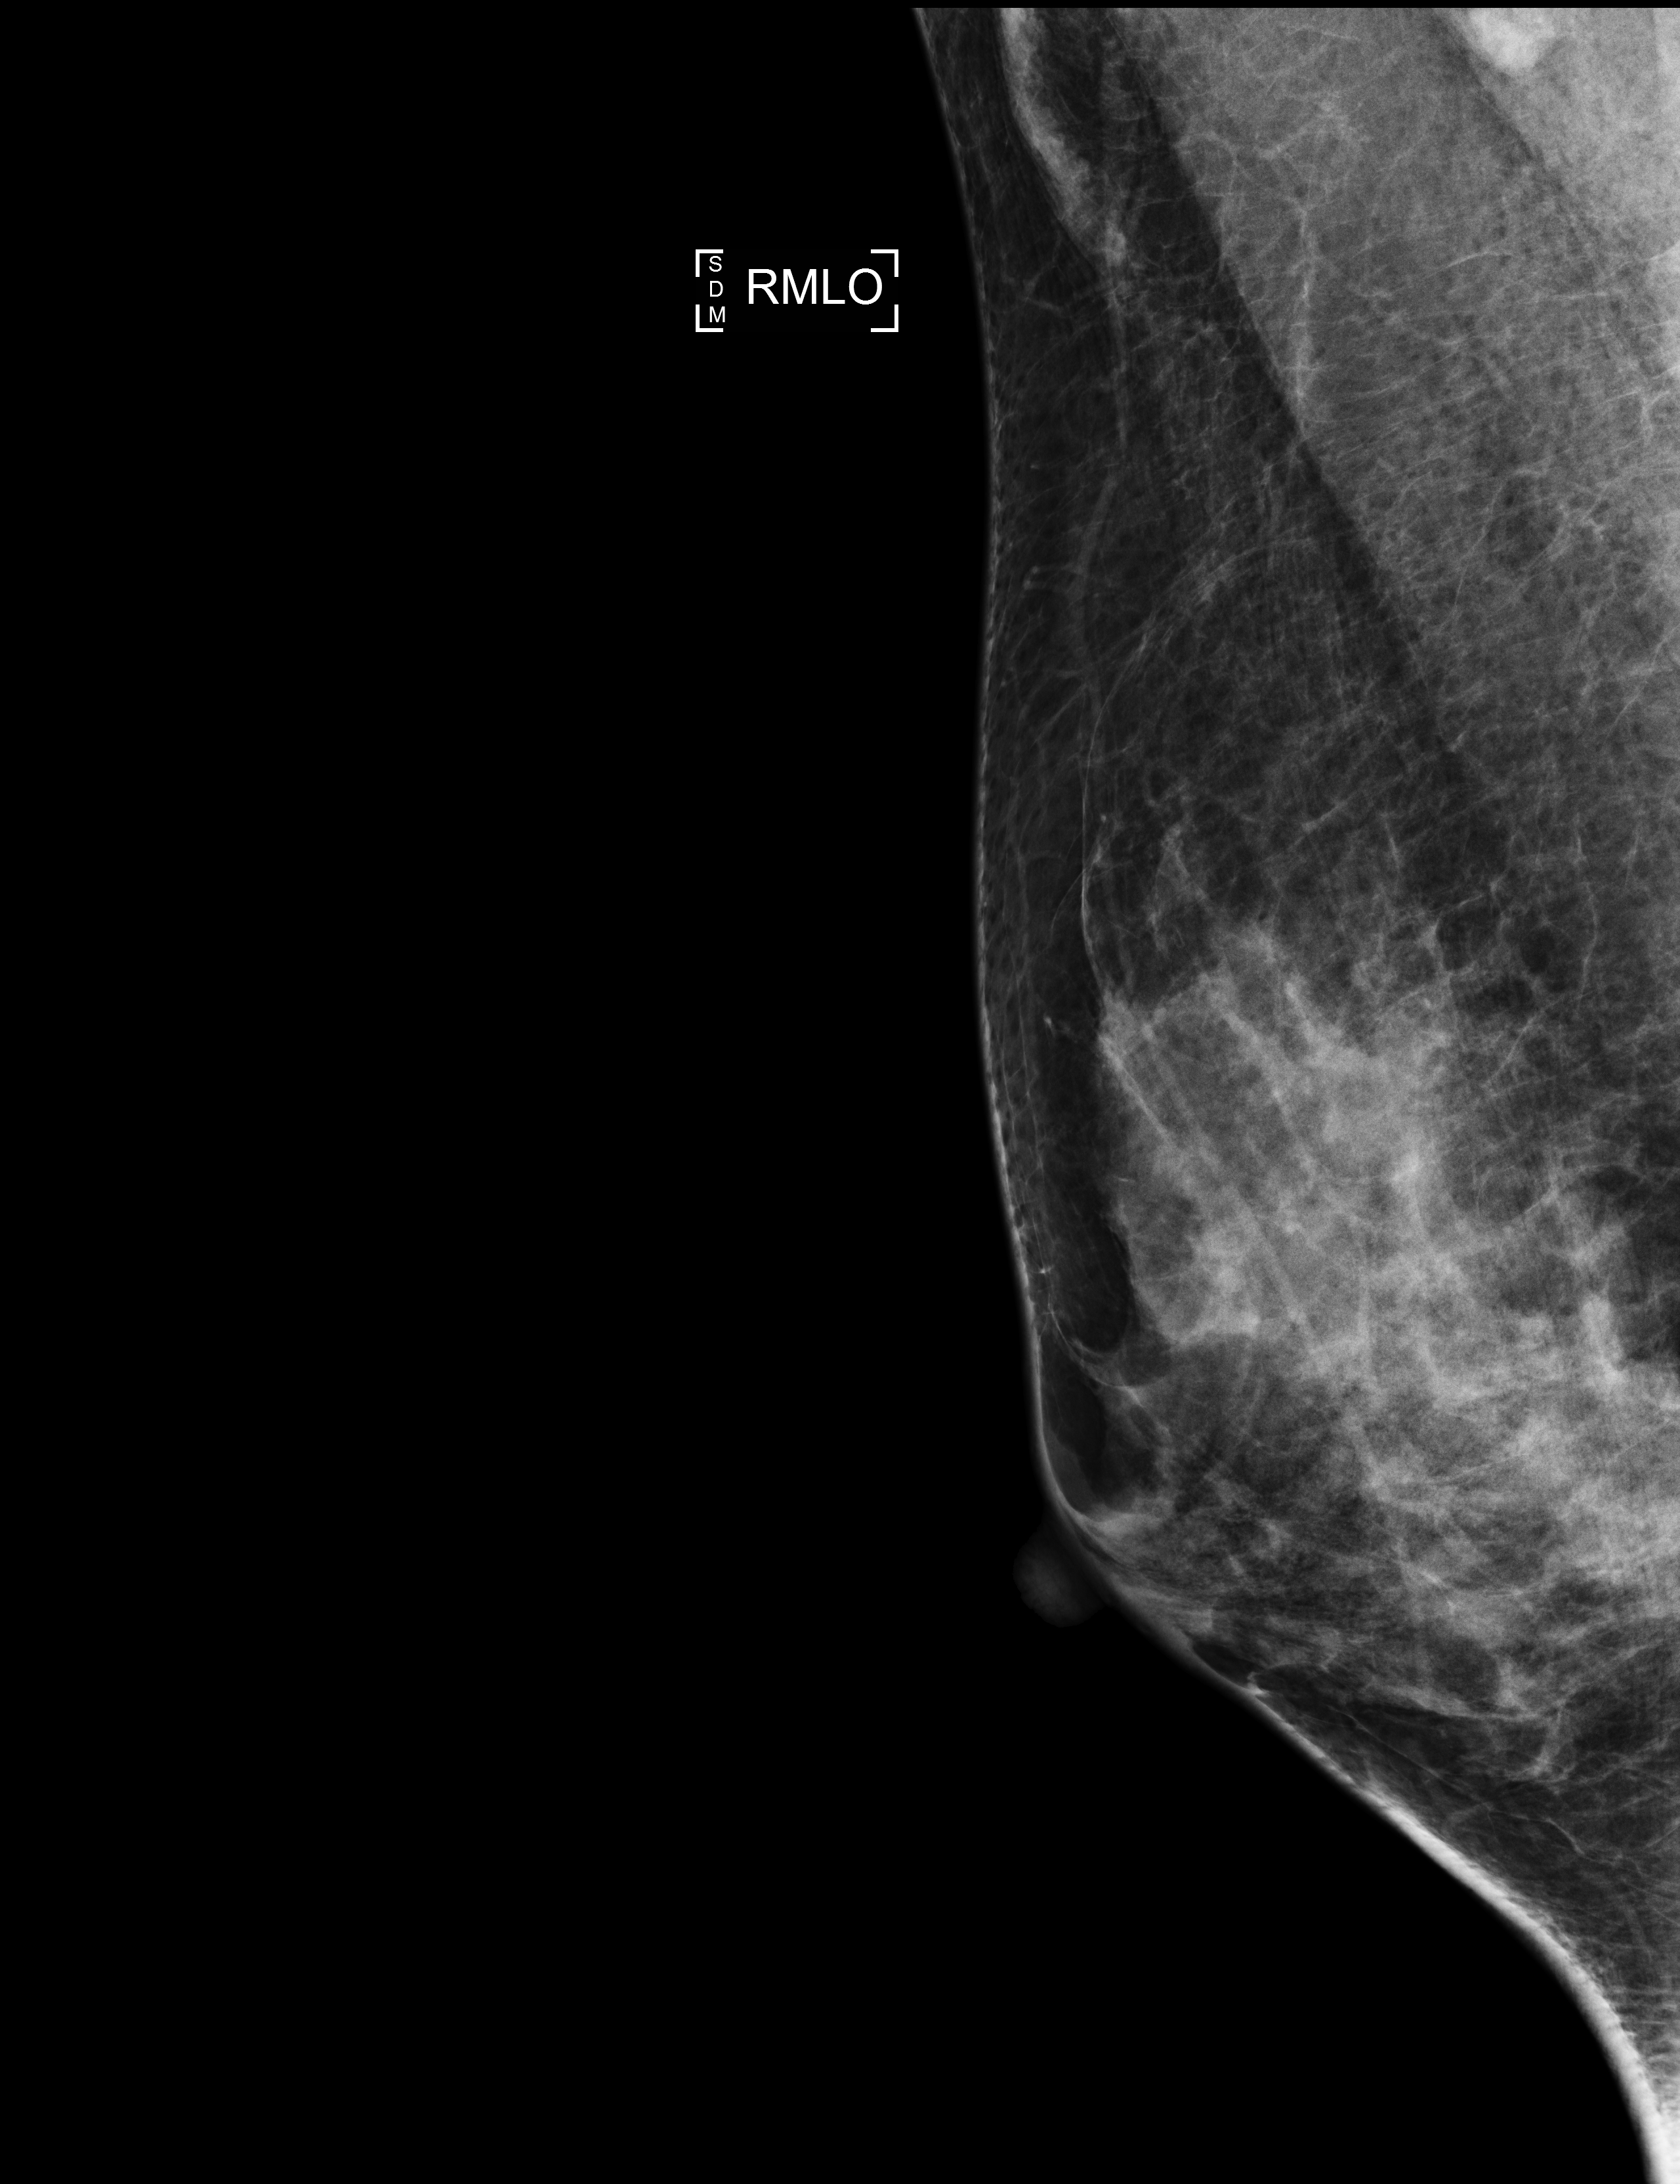
Screening examination; compressed breast thickness 55 mm; system: Selenia Dimensions. Patient aged 43 years (female).
Image type: full-field digital mammogram. Breast: right. Projection: mediolateral oblique (MLO) view.